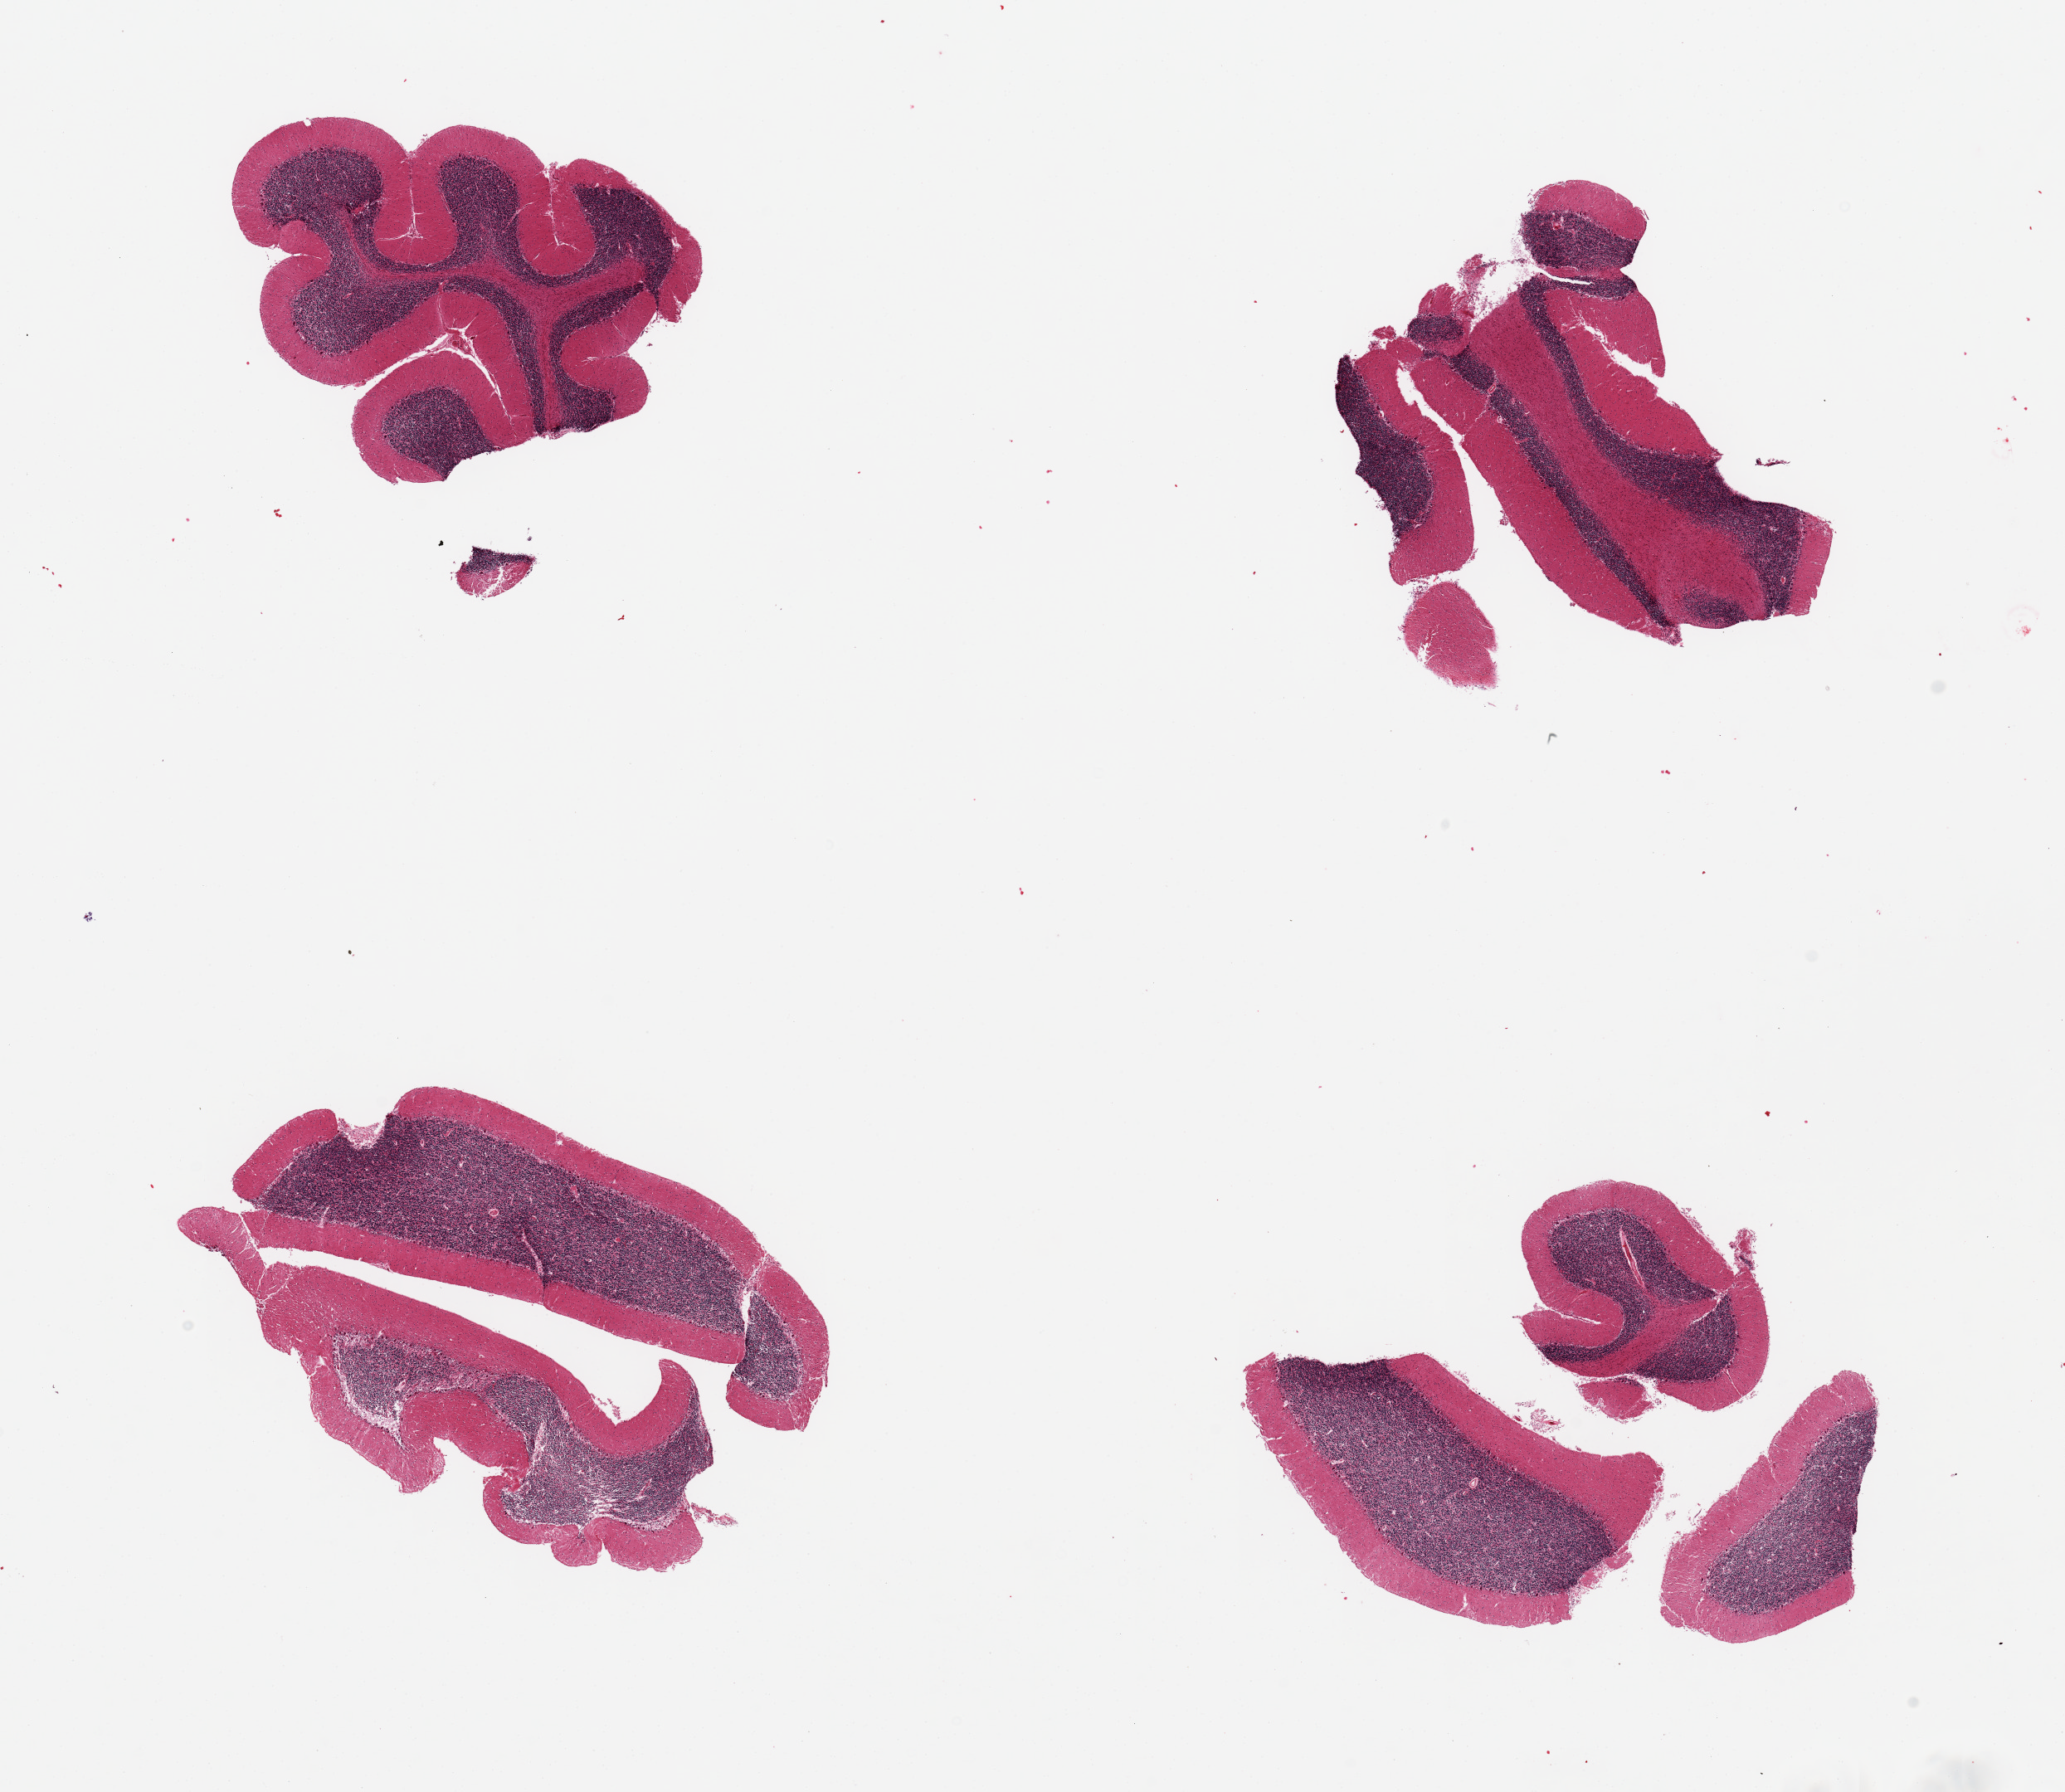
Hematoxylin and eosin (H&E) whole-slide image, whole scanned area (about 19.7 x 17.1 mm, from a 20x scan) shown as a low-resolution overview. PAXgene-fixed, paraffin-embedded tissue. Target tissue: cerebellum. Tissue donor sample. Male donor.
• reviewer comment on this tissue sample: 4 pieces